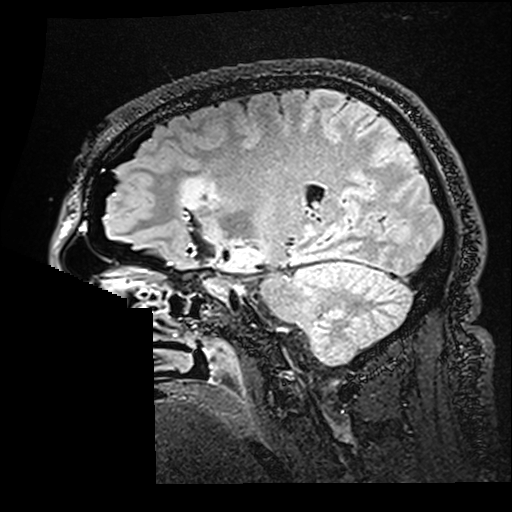
Brain MRI from a brain-tumour surgery series, one sagittal slice. Position 109 of 176 along the scan axis. T2 FLAIR. 1 mm slice thickness. 512 × 512 image matrix, field of view 250 × 250 mm. From the clinical record (not read from this slice): histopathology: Astrocytoma; WHO grade: 2; IDH mutation: yes; tumour location: Right Insular.
Outlined on this slice (outlined manually by an expert reader):
- residual tumour: bounding box [x1, y1, x2, y2] px = [180, 179, 218, 209]